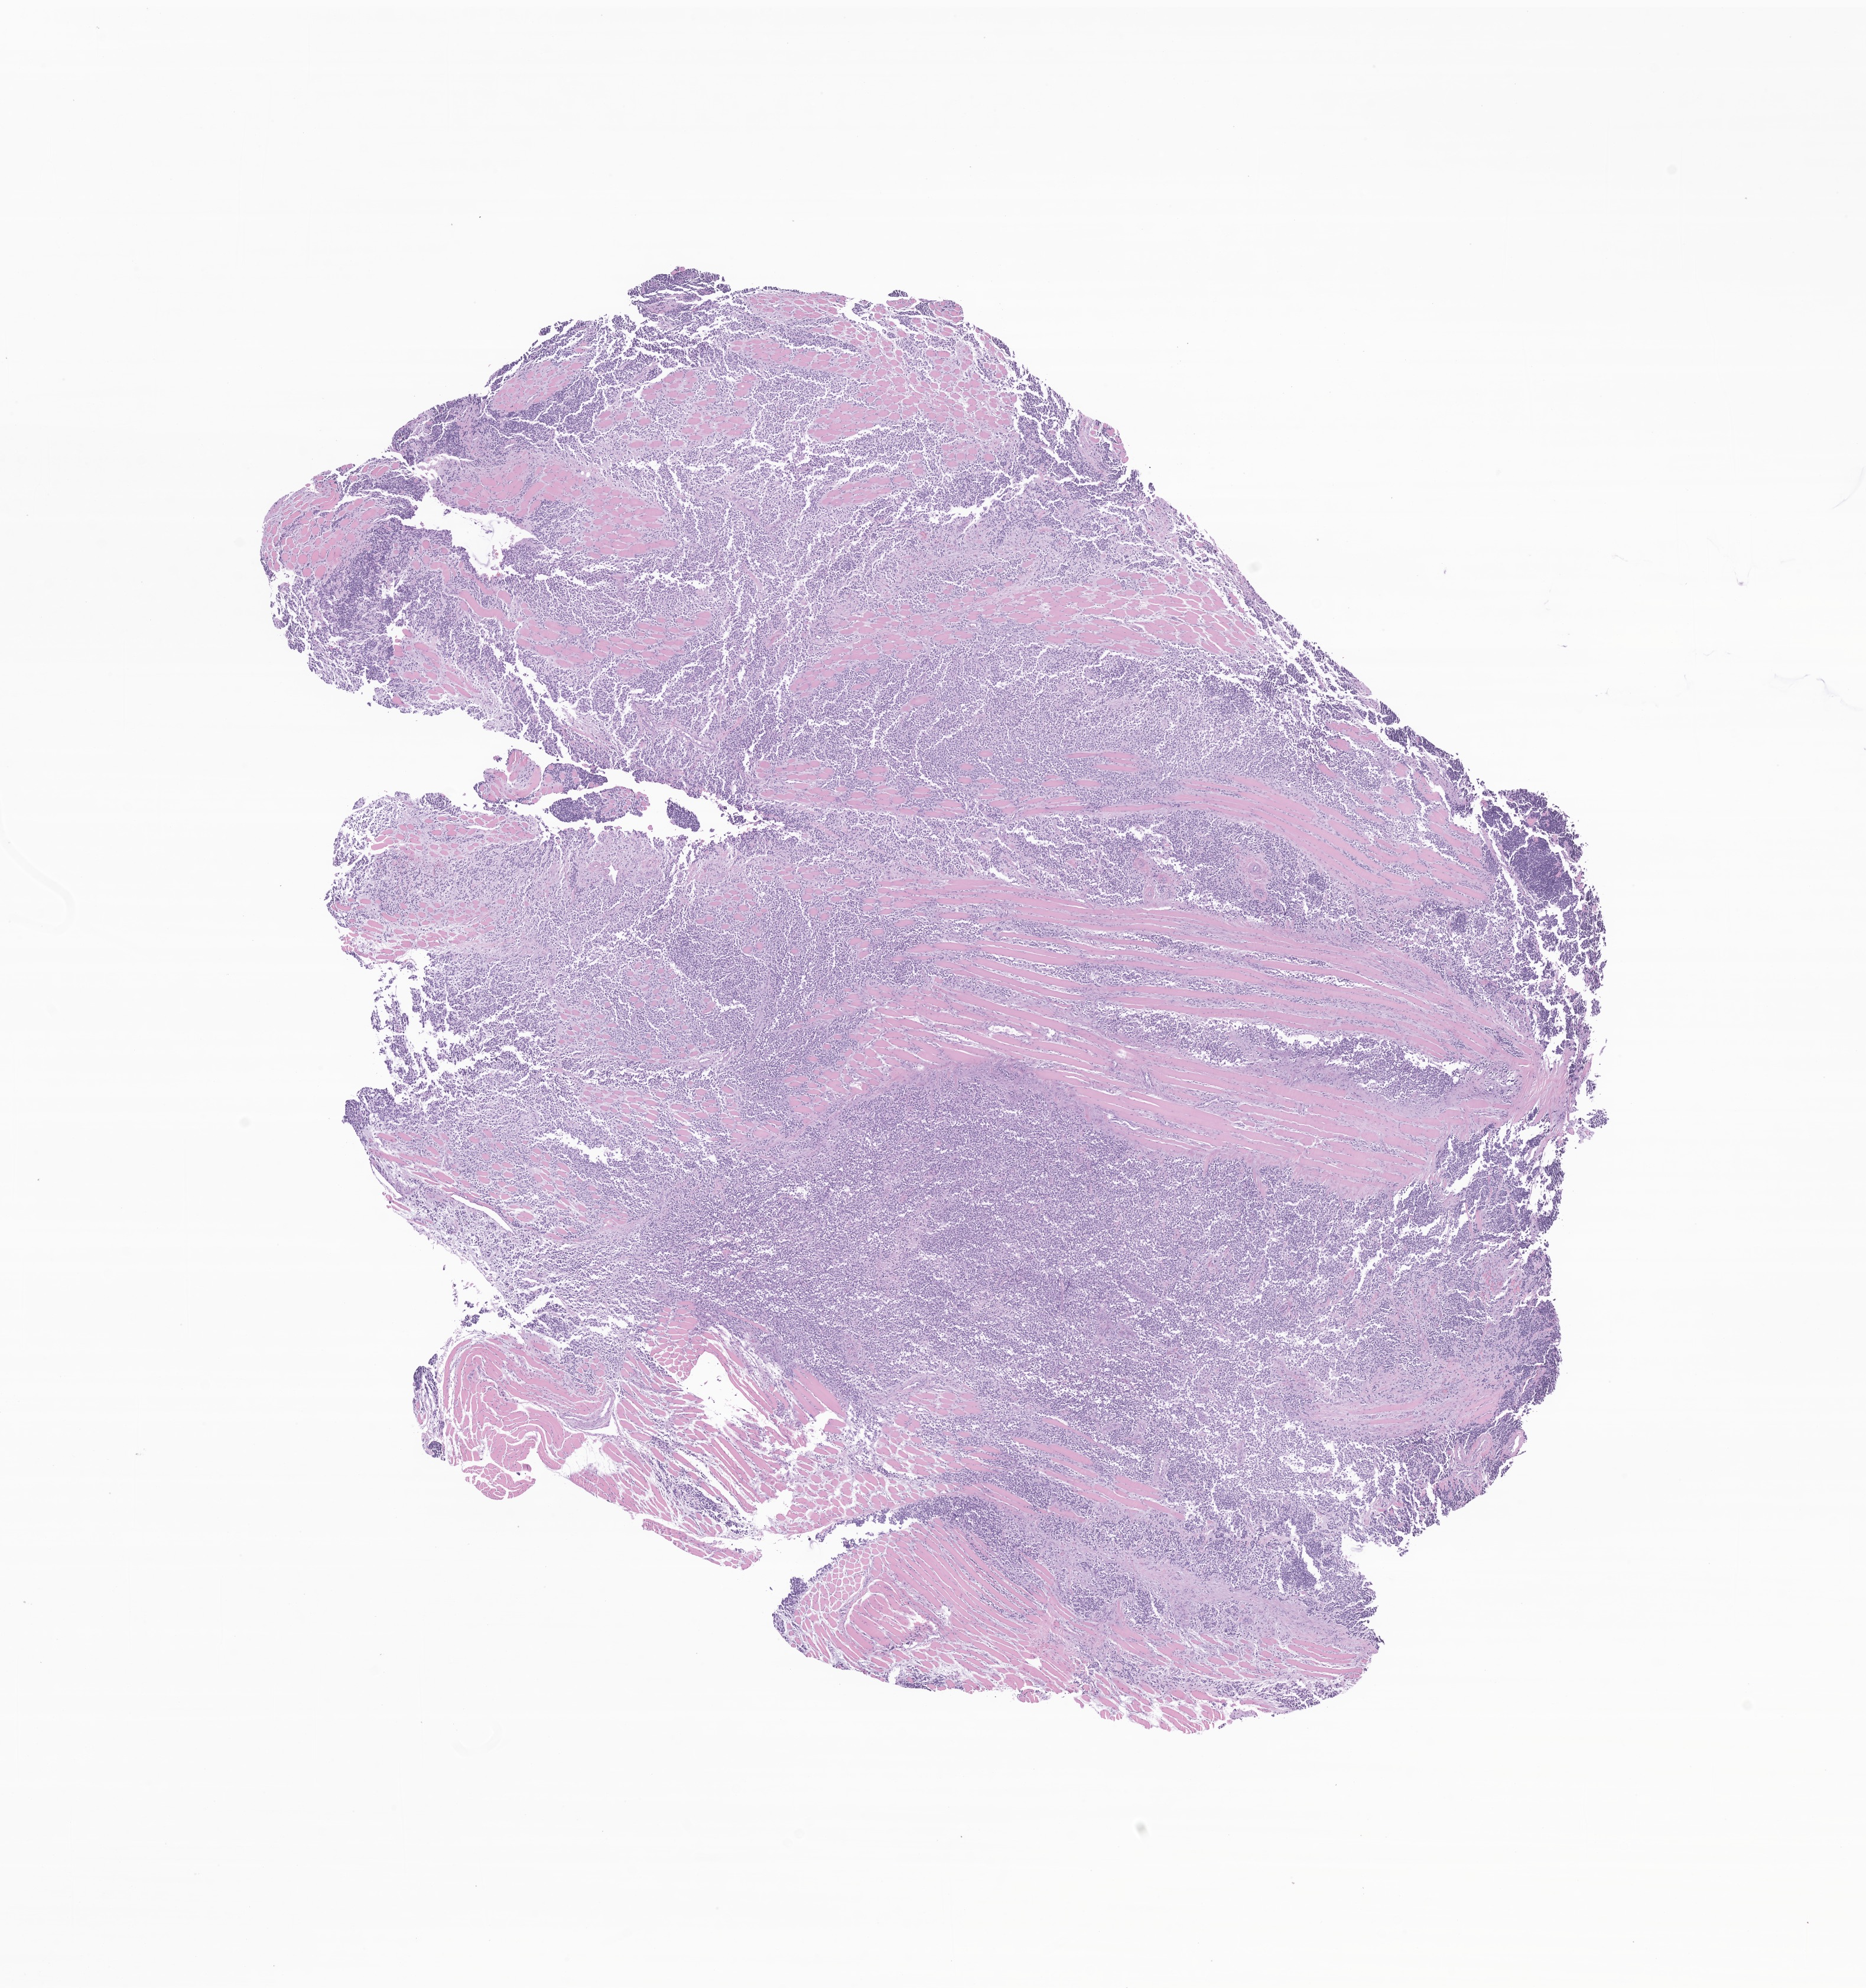
Whole-slide image, hematoxylin and eosin (H&E) stain of tumor tissue from the orbit, whole scanned area (about 13.3 x 14.2 mm) shown as a low-resolution overview, FFPE section. Patient female; age 200 months (16 years 8 months).
* diagnosis (ICD-O-3 morphology term): Alveolar rhabdomyosarcoma